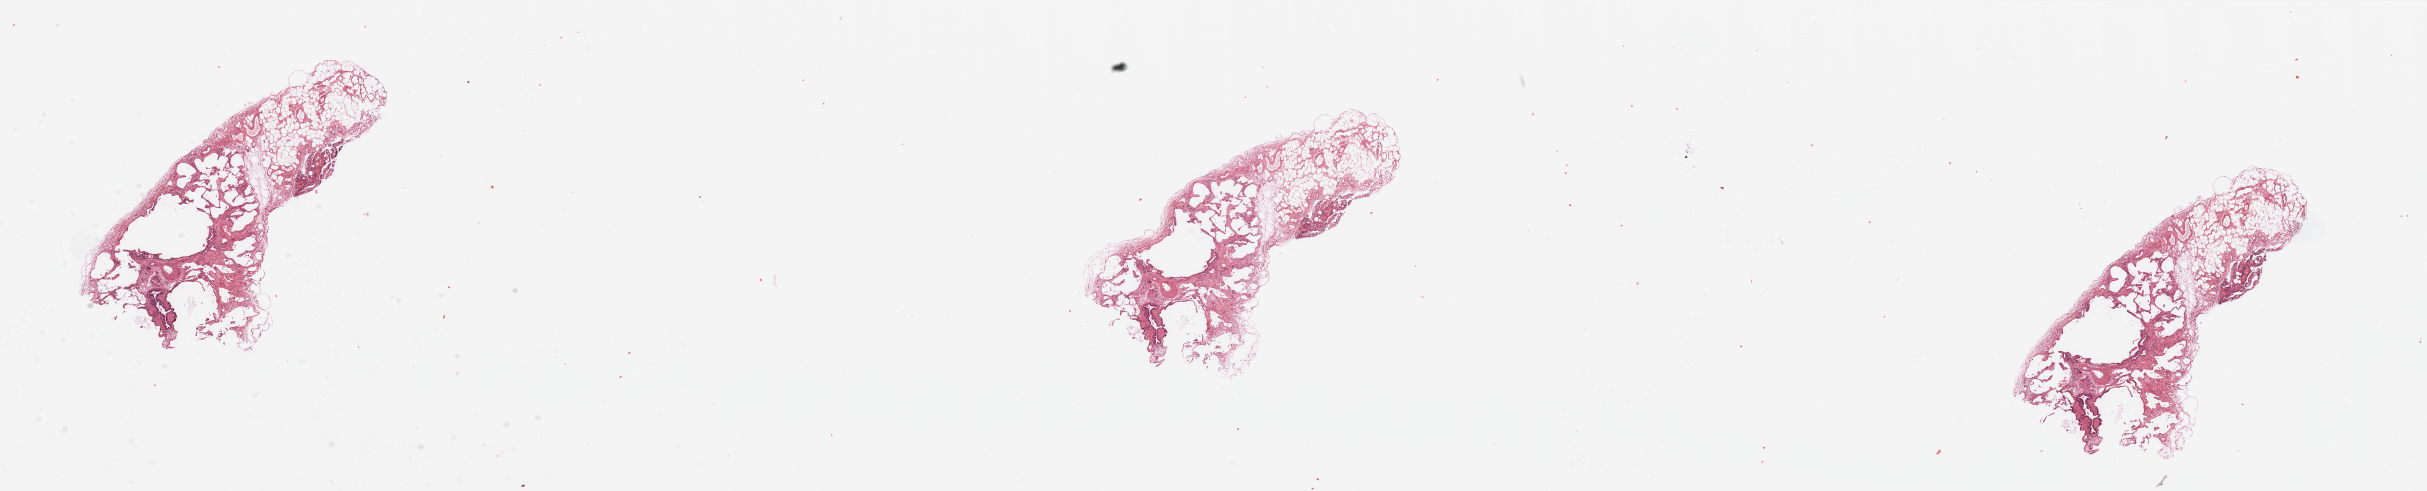
H&E whole-slide image, whole scanned area (about 38.4 x 7.8 mm, acquisition: 20x scan) shown as a low-resolution overview, normal (non-tumour) tissue sample, sampled site: lung. 74-year-old male patient.
This section: normal (non-tumour) tissue from the same patient. Patient diagnosis: Squamous cell carcinoma, NOS.